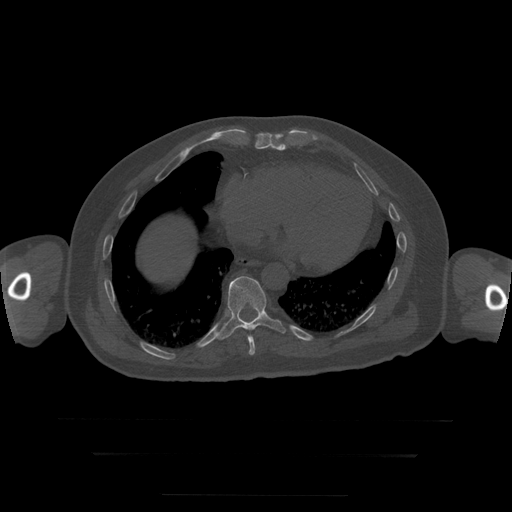
CT including the spine, one axial slice; position 127 of 397 along the scan axis; reconstruction kernel STANDARD; 120 kVp; bone window (W 1800 / L 400 HU); 1.25 mm slice thickness; 512 × 512 image matrix. Patient age 73 years. From the clinical record (not read from this slice): primary cancer: prostate.
Annotated regions visible in this slice (semi-automatically segmented with operator editing):
- T10 vertebra: bounding box [x1, y1, x2, y2] px = [217, 276, 286, 340]
- T9 vertebra: [248, 336, 256, 356]